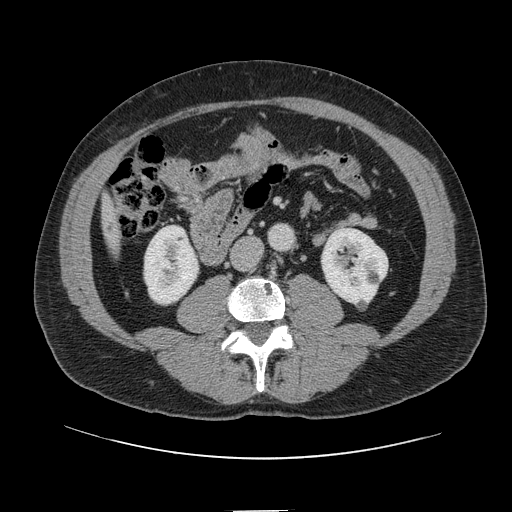
Contrast-enhanced abdominal CT, one axial slice; slice 11 of 161 in the series (ordered by position); intravenous contrast given; soft-tissue window (W 400 / L 40 HU); 2.5 mm slice thickness; 512 × 512 image matrix, field of view 412 × 412 mm. Male patient, age 66 years. Case-level facts recorded for this patient, not image findings: diagnosis: colorectal cancer liver metastases, imaged before liver resection; multiple liver metastases: no; largest metastasis: 3.5 cm; disease in both lobes: no.
Outlined on this slice (outlined manually by an expert reader):
- liver: bounding box [x1, y1, x2, y2] px = [105, 201, 119, 249]
- planned liver remnant (the part of the liver to remain after resection): [105, 202, 117, 236]